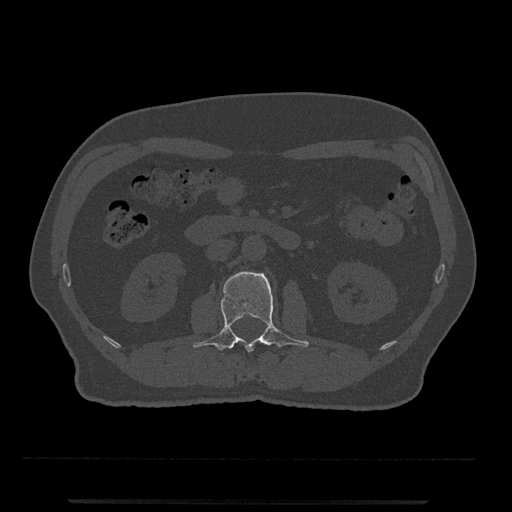
CT including the spine, one axial slice. Slice 272 of 797 in the series (ordered by position). Reconstruction kernel Br40s/3. 120 kVp. Bone window (W 1800 / L 400 HU). 0.5 mm slice thickness. 512 × 512 image matrix. Male patient, age 63 years. Case-level facts recorded for this patient, not image findings: primary cancer: prostate.
Annotated regions visible in this slice (semi-automatically segmented with operator editing):
- L2 vertebra: box from (x=193, y=271) to (x=309, y=352) px